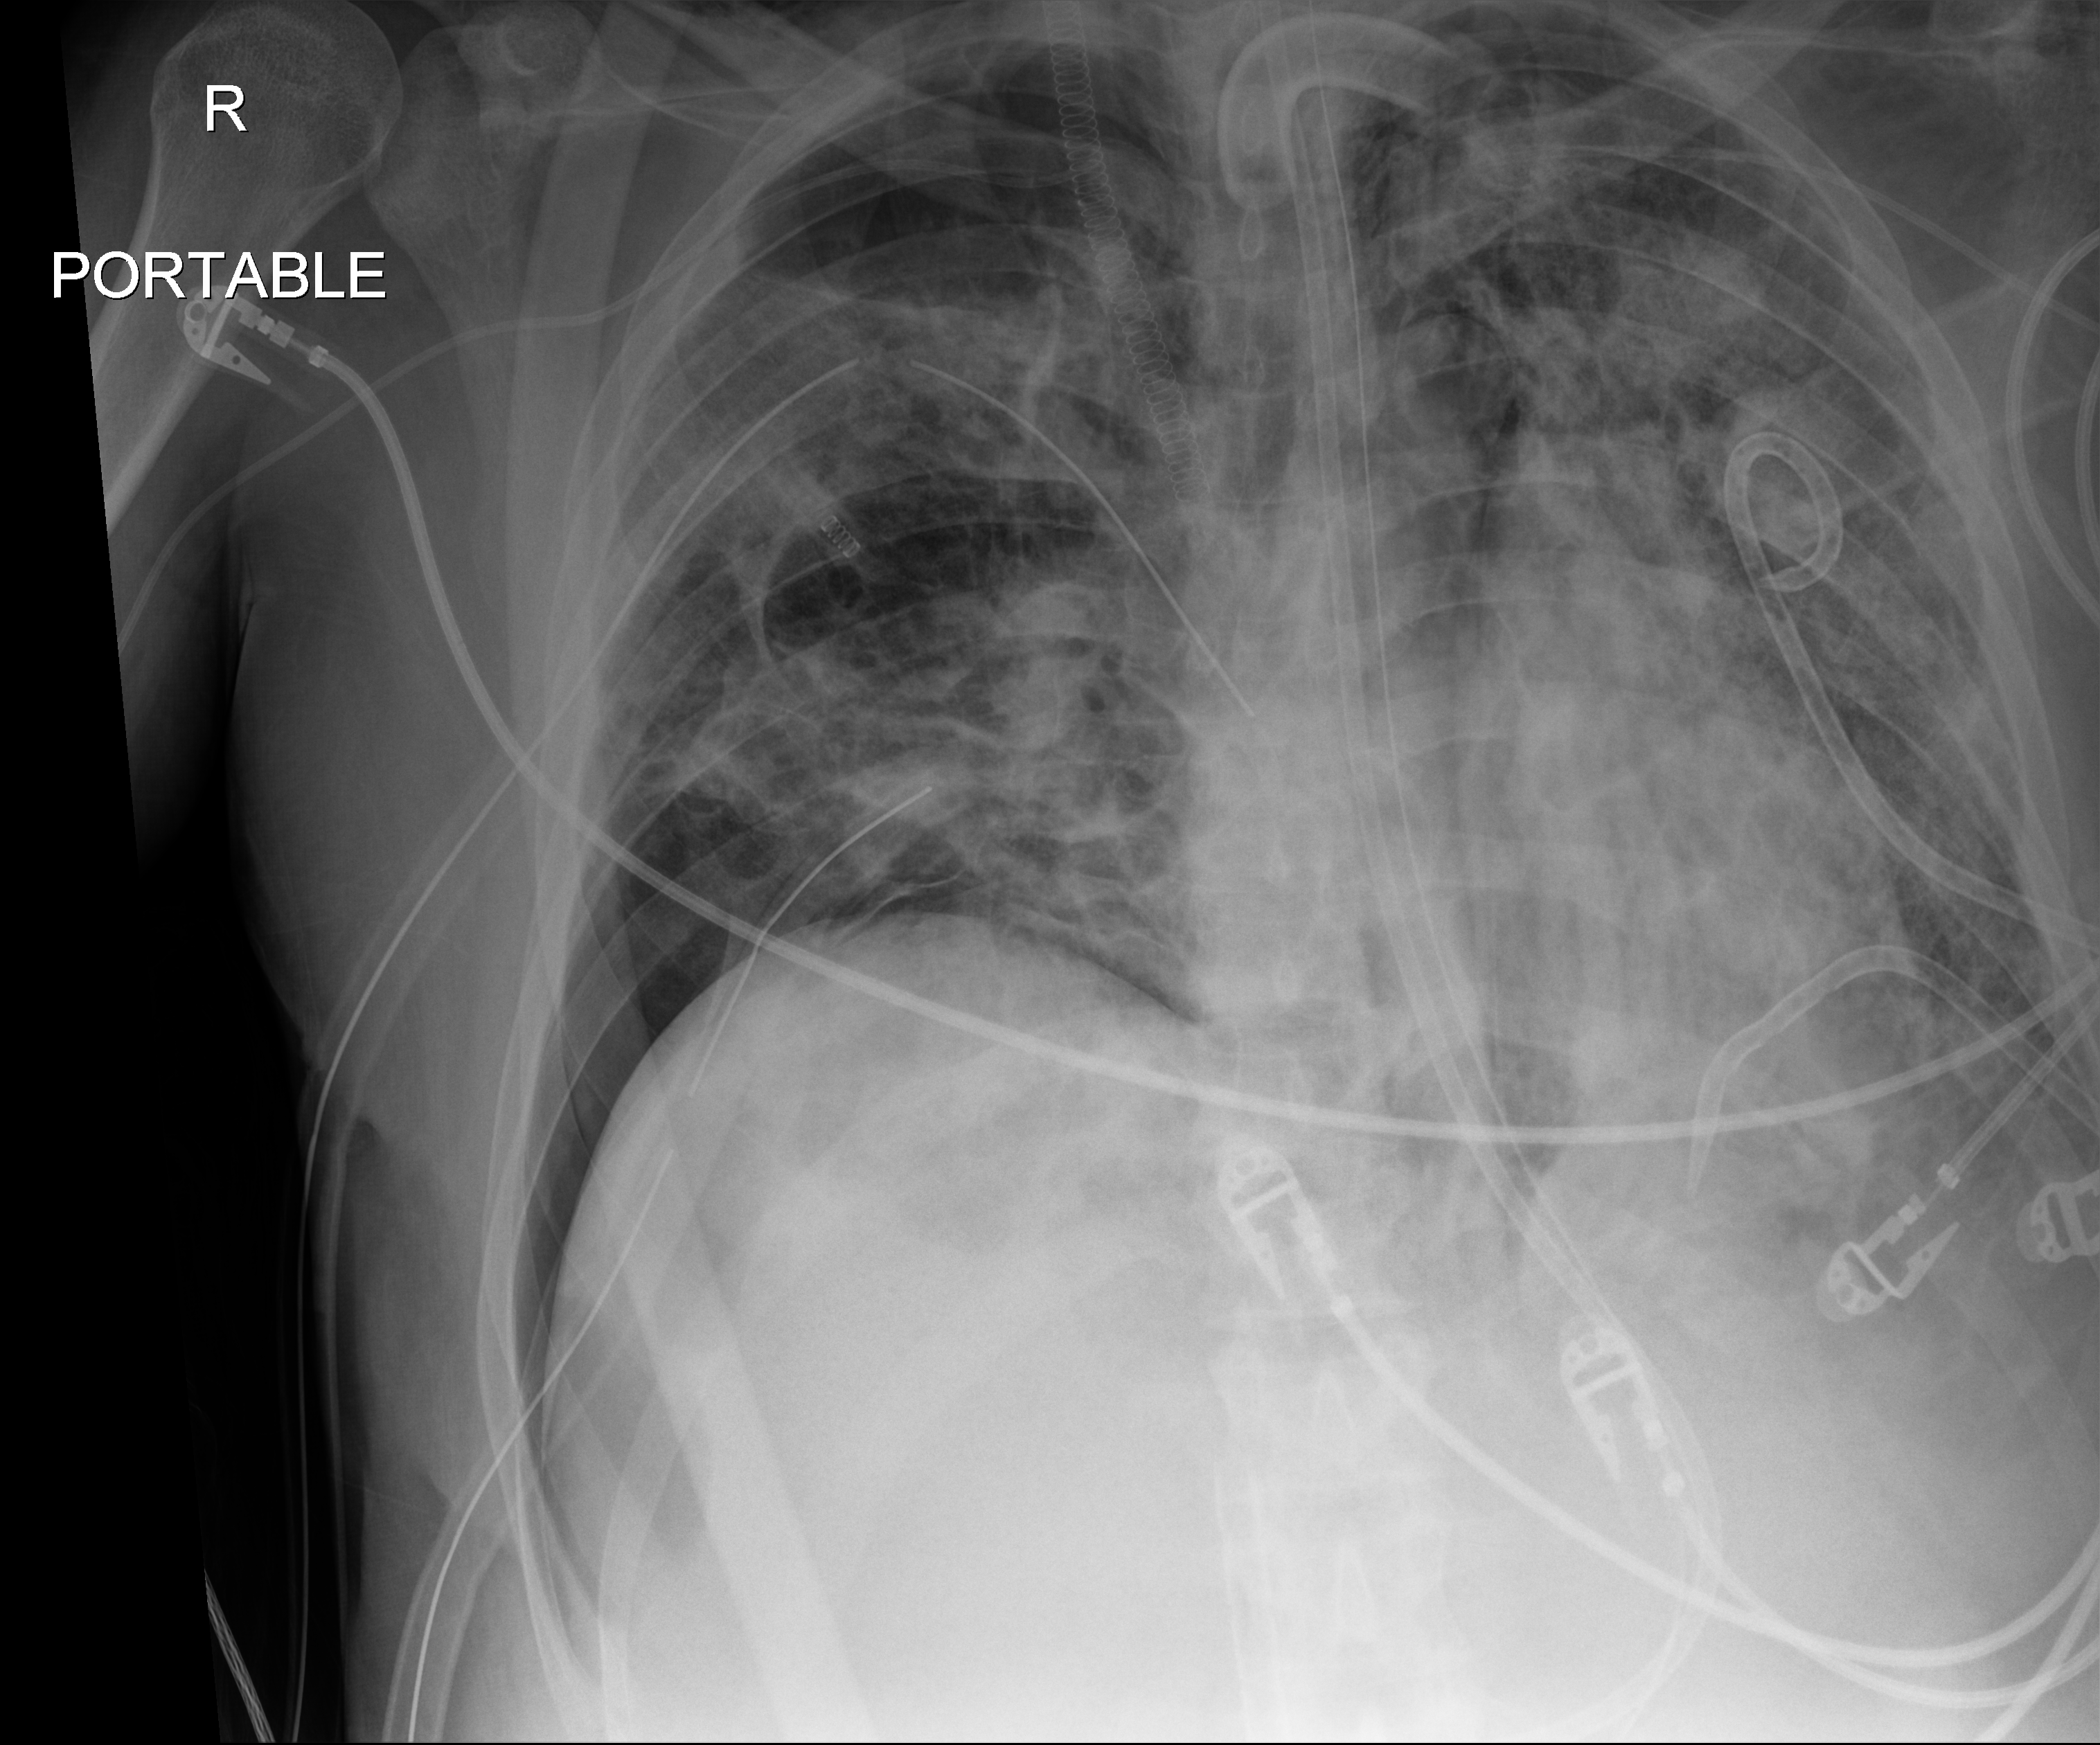
Chest X-ray; anteroposterior (AP) projection. Patient hospitalised with COVID-19, aged 18–59 years.
Admission-level facts for this patient (not findings on this image; timing relative to this image not recorded): admitted to intensive care during this hospital stay: yes; hypertension (admission record): no; mechanically ventilated during this hospital stay: yes.